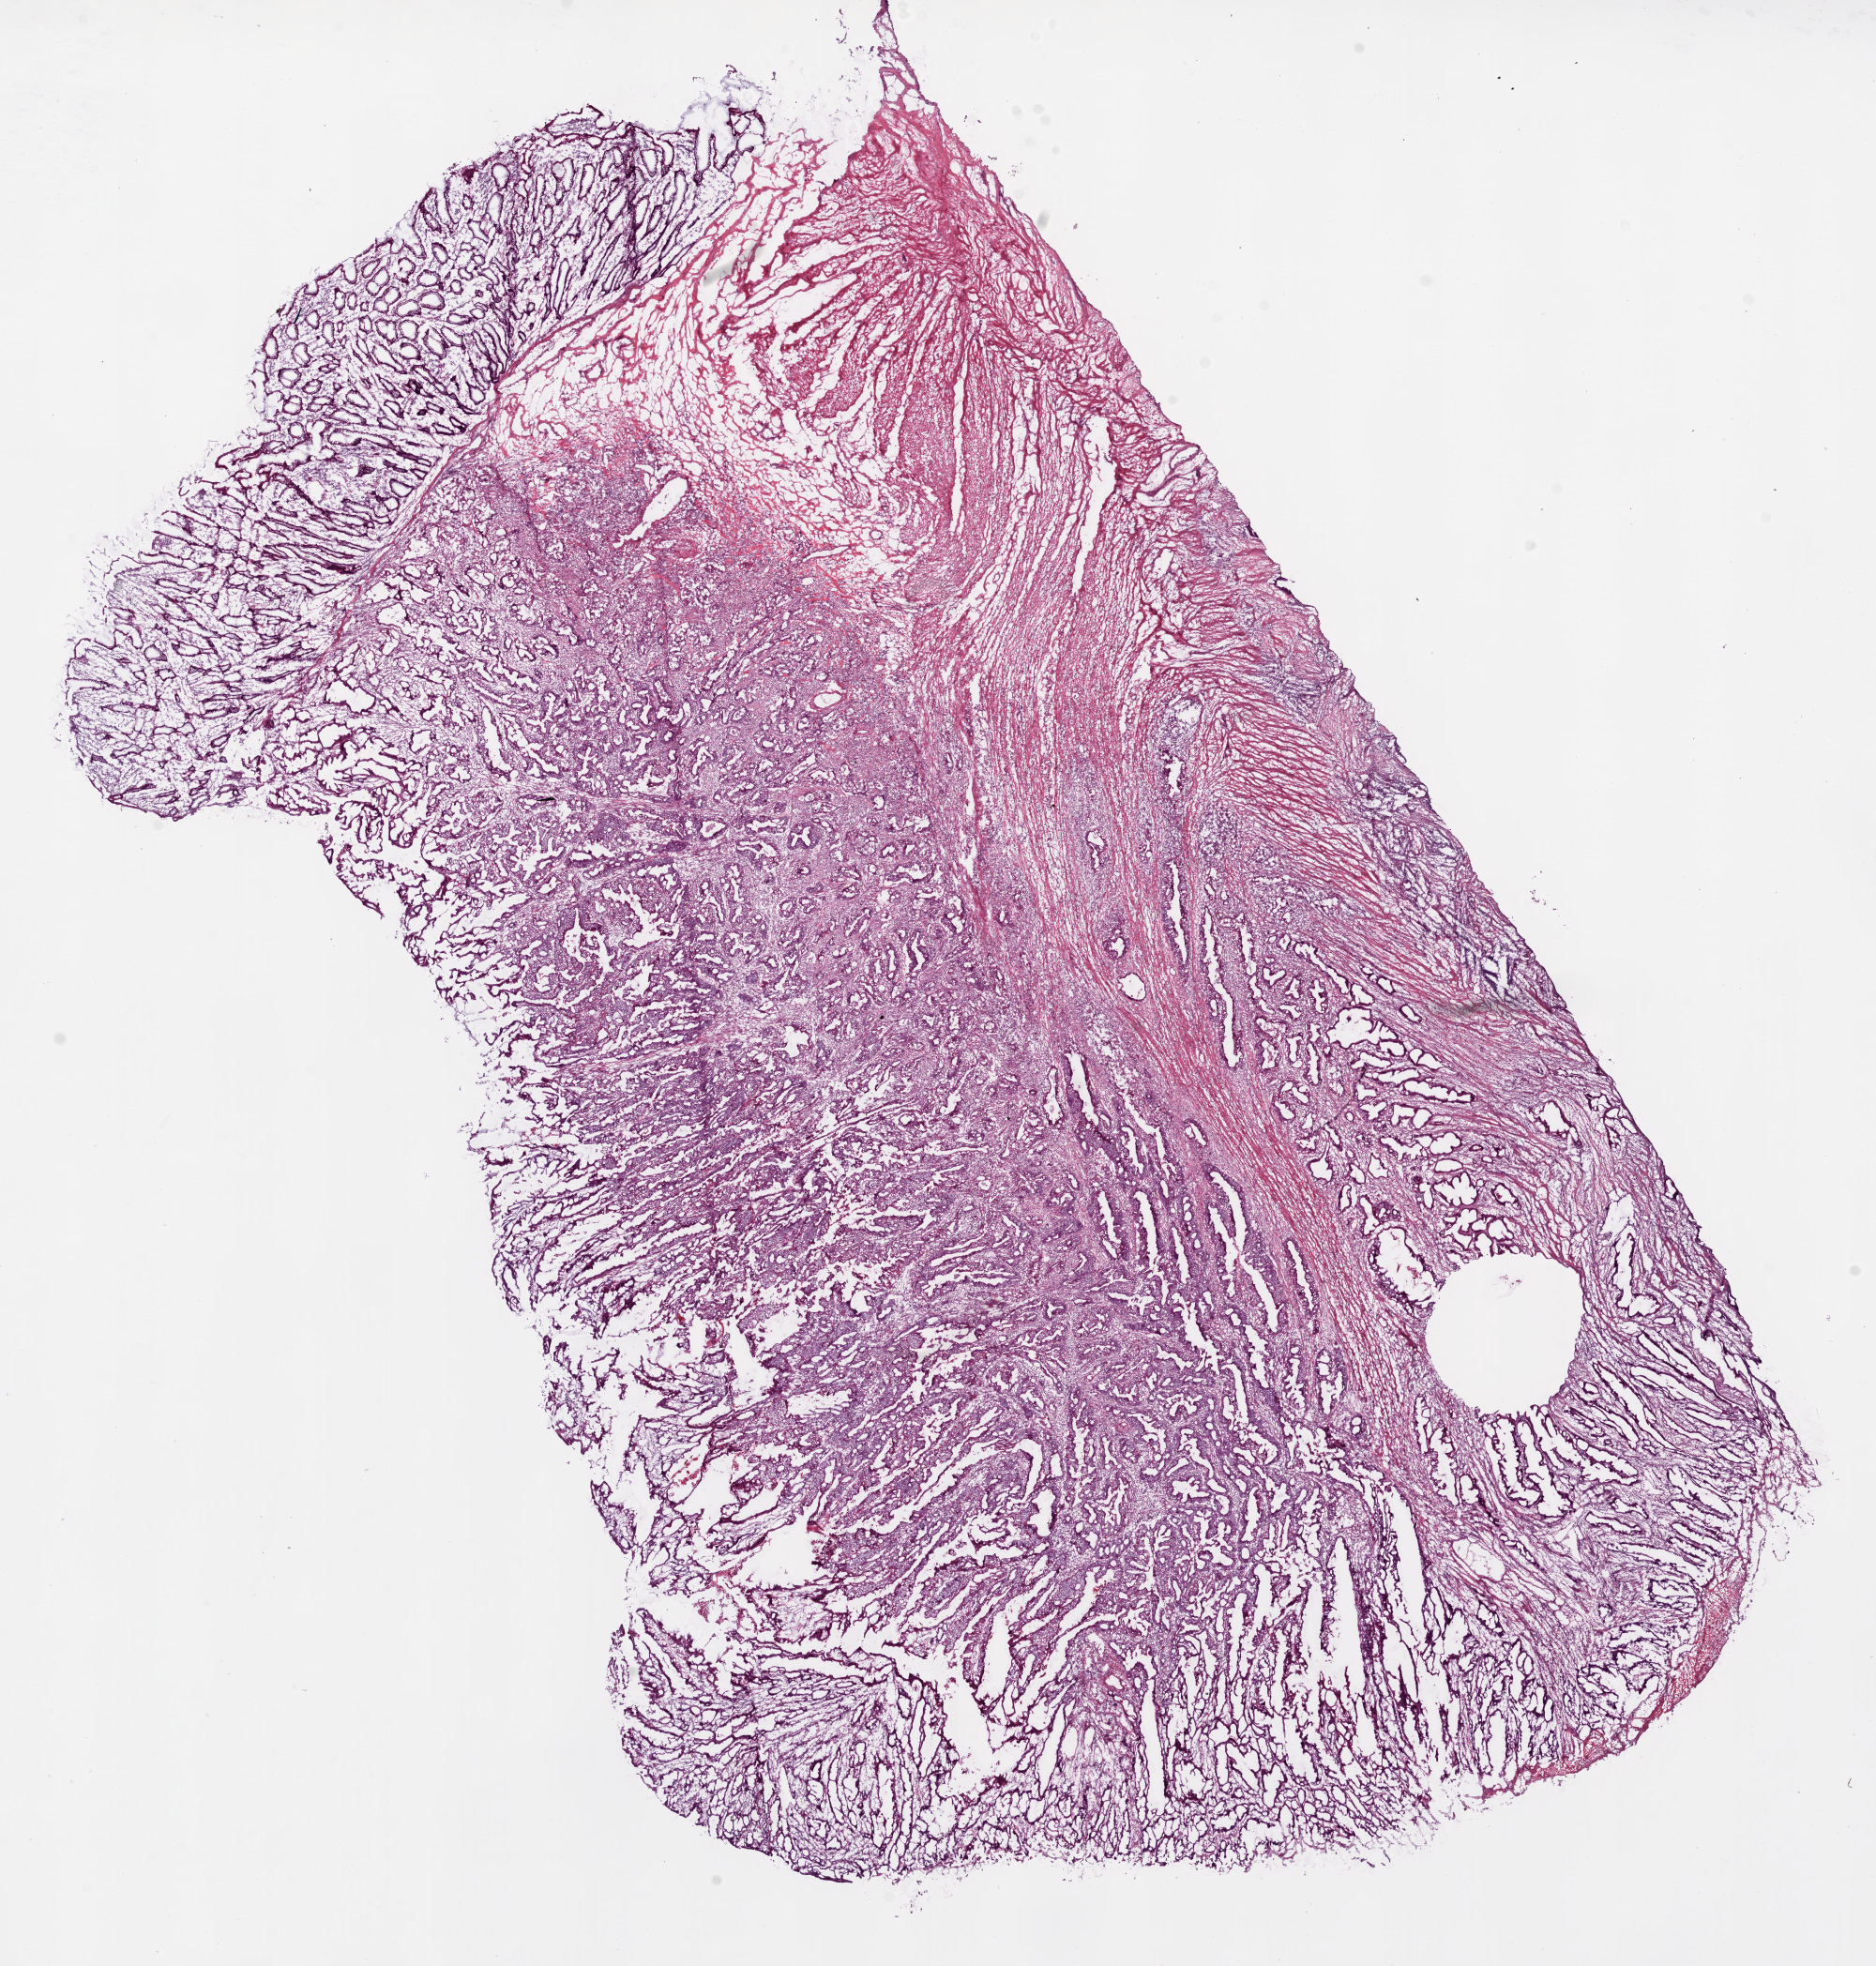
Digitized Hematoxylin and eosin (H&E) stained tissue section (whole slide), whole scanned area (about 16.0 x 16.8 mm, acquisition: 20x scan) shown as a low-resolution overview, frozen section, sample: primary tumour, colon. Patient: male, age at initial diagnosis 45 years. Composition of this section per pathologist review: tumour cells 53%, tumour nuclei 70%, normal cells 10%, stromal cells 30%, necrosis 3%.
• diagnosis: Adenocarcinoma, NOS
• AJCC pathologic stage: IIA (6th edition)
• TNM: T3 N0 M0